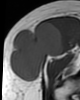
MRI of an extremity soft-tissue mass, one axial slice. Position 23 of 46 along the scan axis. MR volume resampled by the dataset authors to the PET/CT grid (not the native acquisition matrix). 3.27 mm slice thickness. 80 × 100 image matrix. Female patient. Case-level facts recorded for this patient, not image findings: histological type: synovial sarcoma; grade: intermediate; site of the primary tumour: right thigh.
Annotated regions visible in this slice (expert contour drawn on MRI and transferred to this co-registered scan by the dataset authors):
- gross tumour volume including surrounding oedema: bounding box <10,21,65,82> (left, top, right, bottom; pixels)
- gross tumour volume (mass): <10,21,65,82>